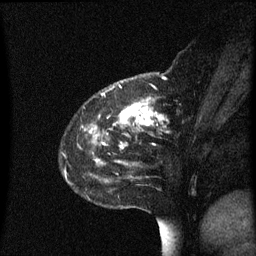
Breast MRI (dynamic contrast-enhanced), one sagittal slice; position 19 of 60 along the scan axis; dynamic contrast-enhanced series, image 2 of 3 at this slice position (ordered by acquisition); 1.5 T; TE 4.2 ms, TR 8.4 ms; 2 mm slice thickness; 256 × 256 image matrix, field of view 200 × 200 mm. Female patient, age 48 years. From the clinical record (not read from this slice): setting: breast cancer imaged before/during neoadjuvant chemotherapy; receptor status: HR-positive, HER2-negative.
Annotated regions visible in this slice (semi-automatic segmentation, software-assisted and operator-edited):
- analysis volume of interest (the breast-tissue region the enhancement analysis was run in; not a lesion): bounding box (x1, y1, x2, y2) in pixels: (80, 78, 195, 221)
- tumour enhancement mask (voxels above the 70 % enhancement threshold inside the analysis volume of interest): (102, 87, 165, 163)